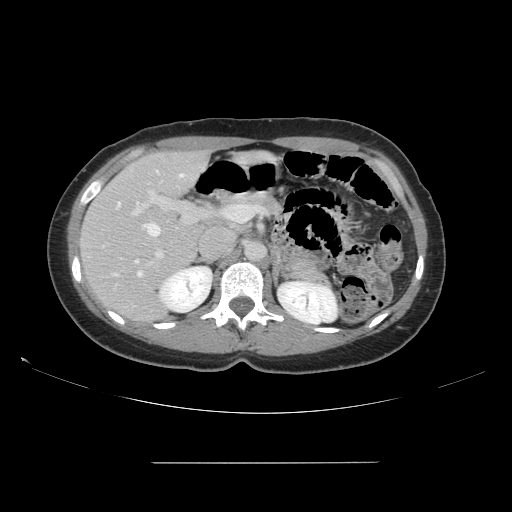
Contrast-enhanced abdominal CT, one axial slice; 120 kVp; intravenous contrast given; soft-tissue window (W 400 / L 40 HU); 2.5 mm slice thickness; 512 × 512 image matrix, field of view 421 × 421 mm. Female patient, age 46 years. From the clinical record (not read from this slice): diagnosis: colorectal cancer liver metastases, imaged before liver resection; multiple liver metastases: yes; largest metastasis: 3 cm; disease in both lobes: yes.
Structures marked on this image (expert manual segmentation):
- hepatic veins: bounding box [x1, y1, x2, y2] px = [114, 171, 185, 277]
- liver: [82, 151, 209, 322]
- planned liver remnant (the part of the liver to remain after resection): [91, 152, 203, 270]
- portal vein (with intrahepatic branches): [131, 181, 247, 266]